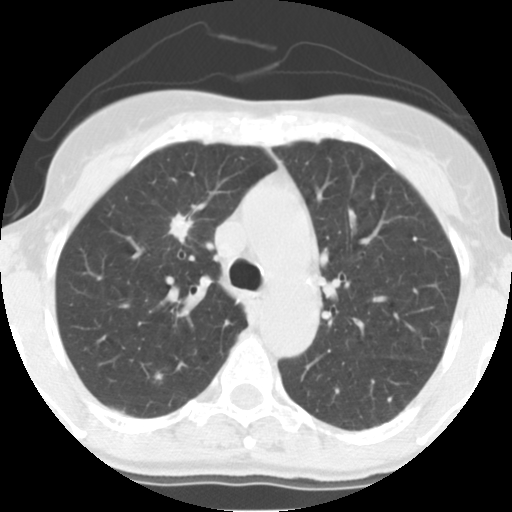
Low-dose screening chest CT, one axial slice; slice 97 of 140 in the series (ordered by position); reconstruction kernel STANDARD; lung window (W 1500 / L -600 HU); 2.5 mm slice thickness; 512 × 512 image matrix, field of view 280 × 280 mm.
Annotated regions visible in this slice (outlined manually by an expert reader):
- lesion 1 (tumor, upper lobe of right lung): bounding box (x1, y1, x2, y2) in pixels: (167, 213, 193, 243)